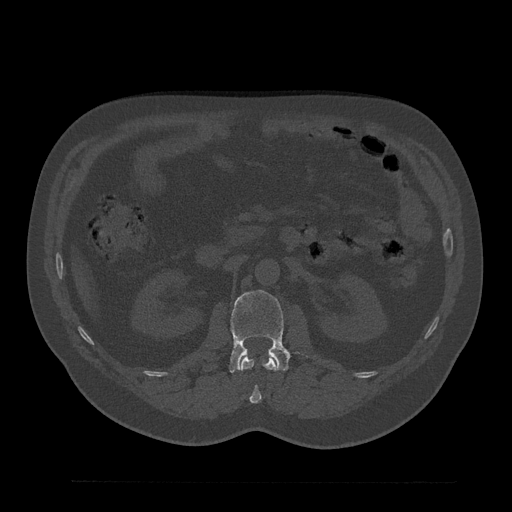
CT including the spine, one axial slice; position 121 of 797 along the scan axis; bone window (W 1800 / L 400 HU); 0.5 mm slice thickness; 512 × 512 image matrix, field of view 430 × 430 mm. Patient: male, 61 years. From the clinical record (not read from this slice): primary cancer: prostate.
Outlined on this slice (semi-automatically segmented with operator editing):
- L1 vertebra: bounding box [x1, y1, x2, y2] px = [240, 355, 278, 404]
- L2 vertebra: [229, 290, 289, 372]